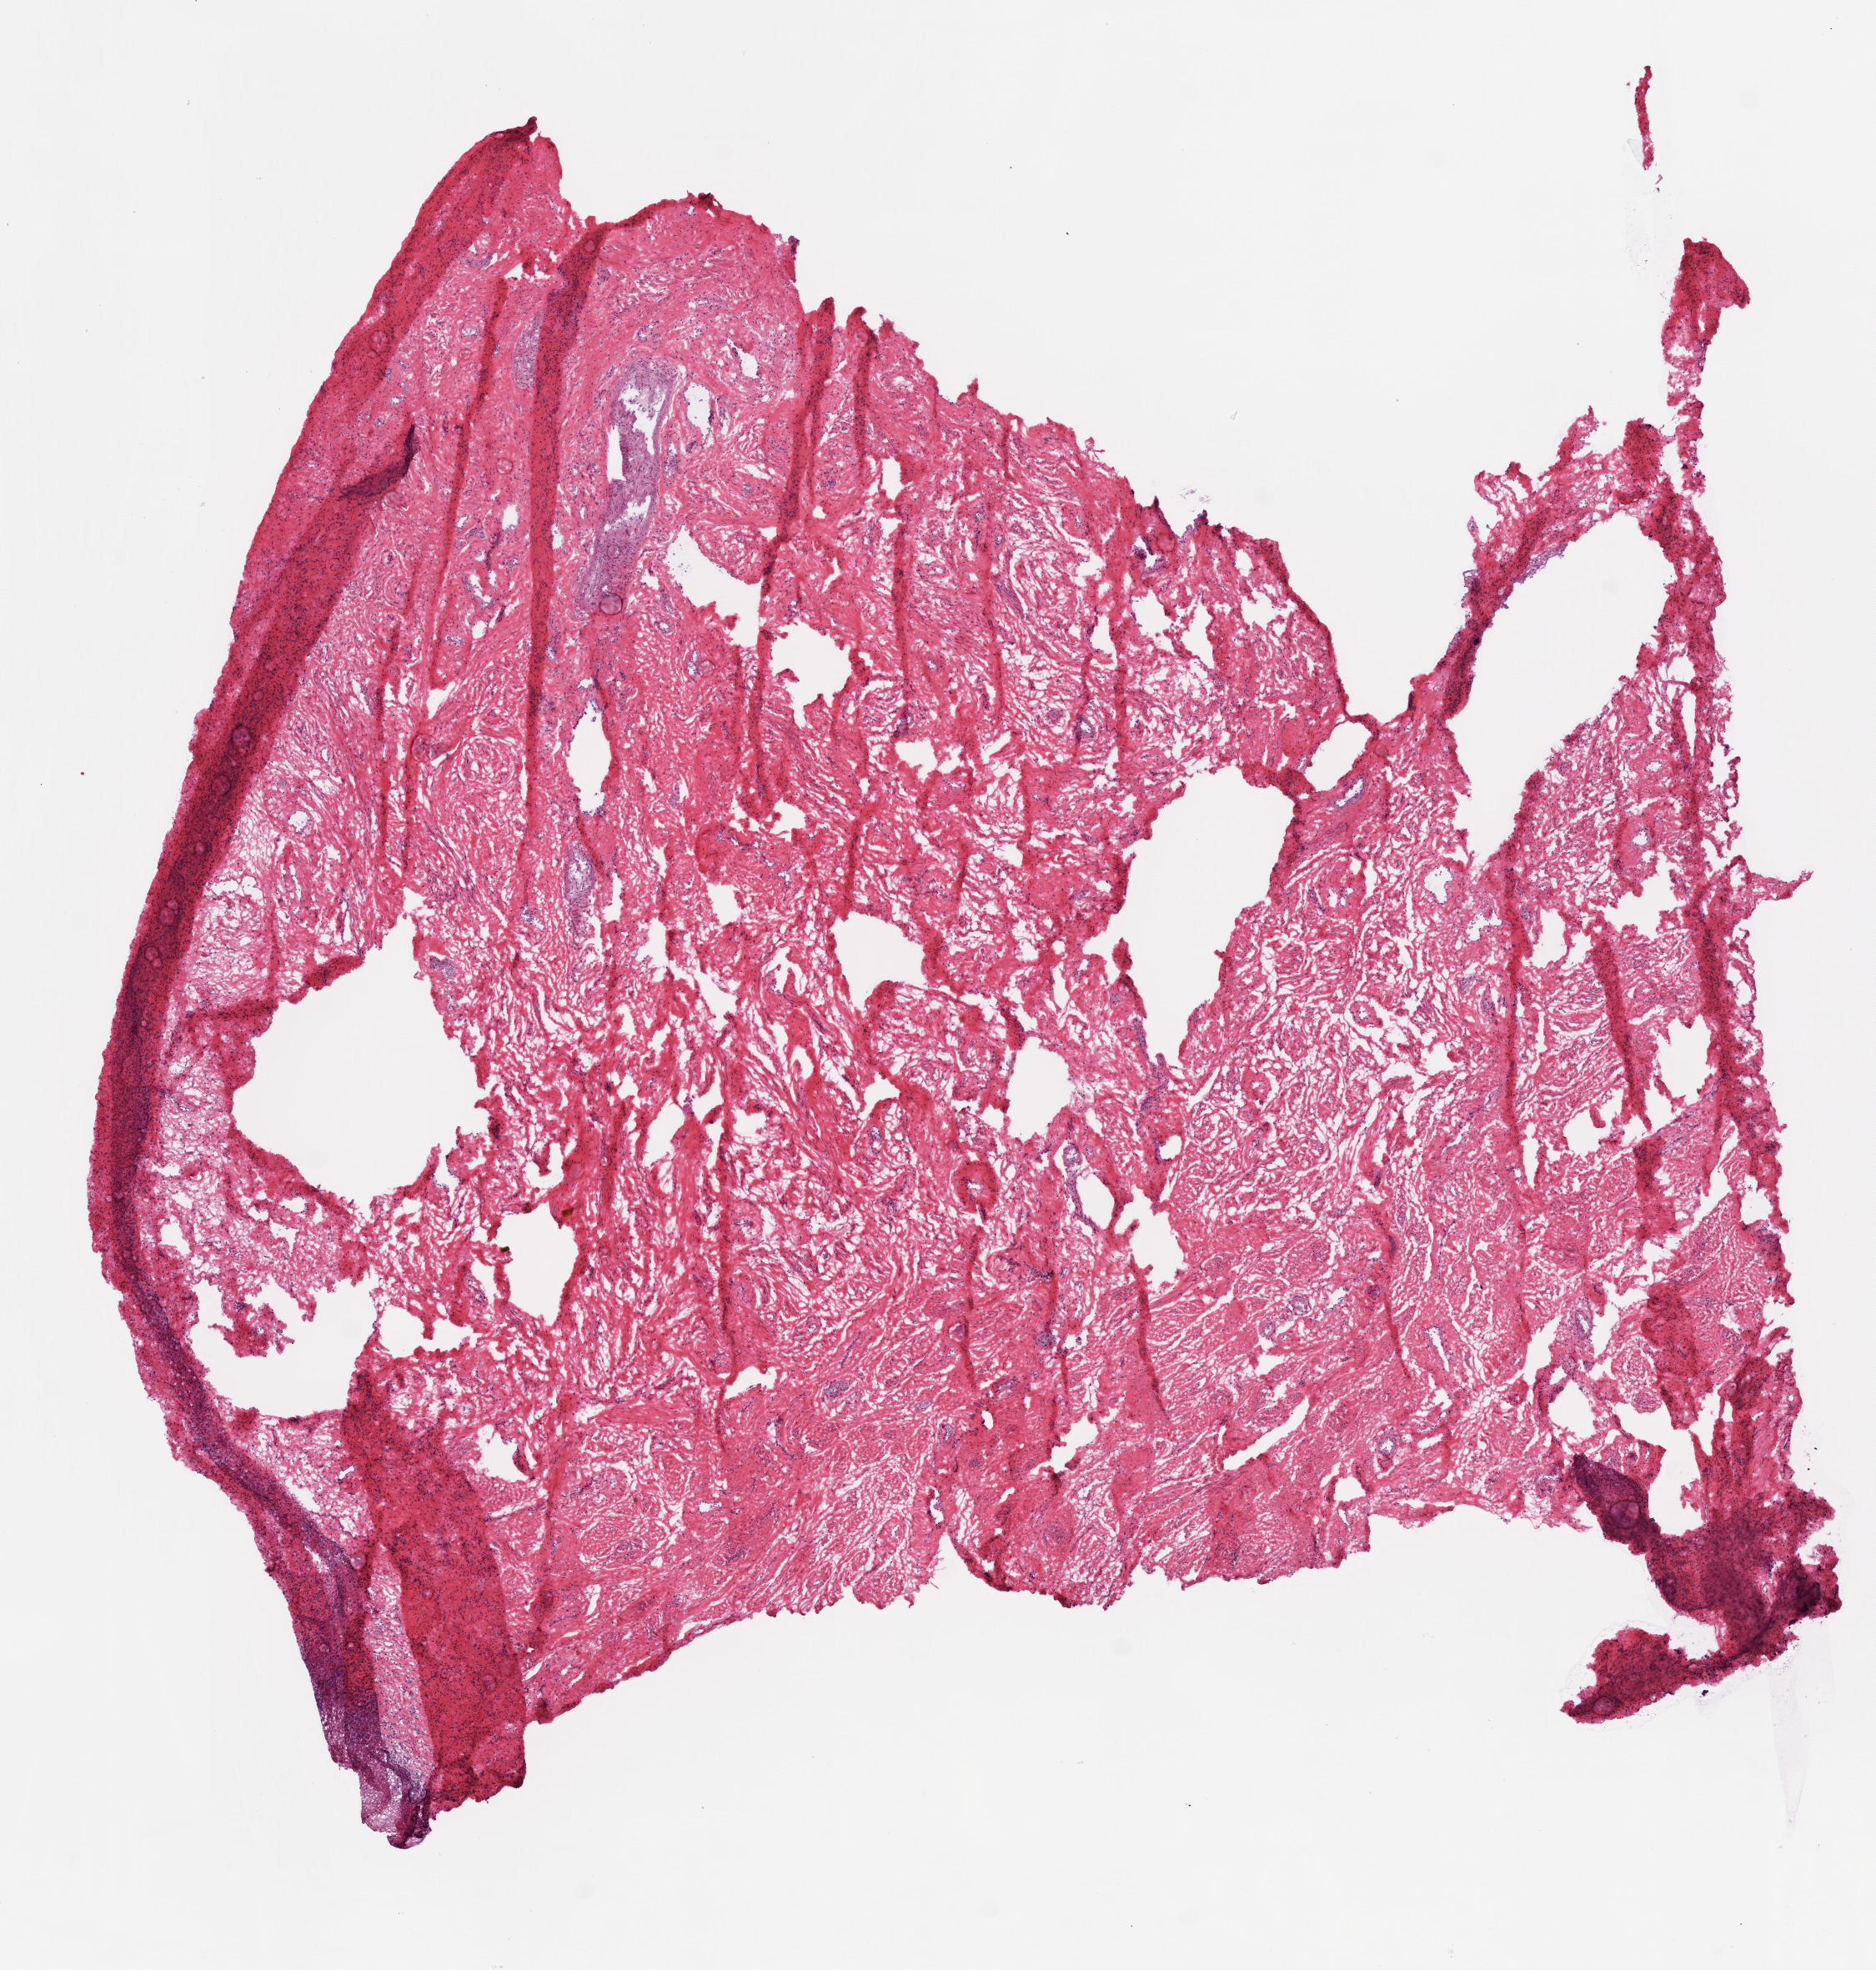
H&E-stained whole-slide image, low-resolution overview of the scanned area, about 9.0 x 9.5 mm (acquisition: 20x scan), frozen section from the top of the tissue portion, ovary, solid tissue normal (non-tumour tissue) sample. Female patient; age at initial diagnosis 53 years.
This section: solid tissue normal sample (biorepository sample class). Patient diagnosis: Serous cystadenocarcinoma, NOS.